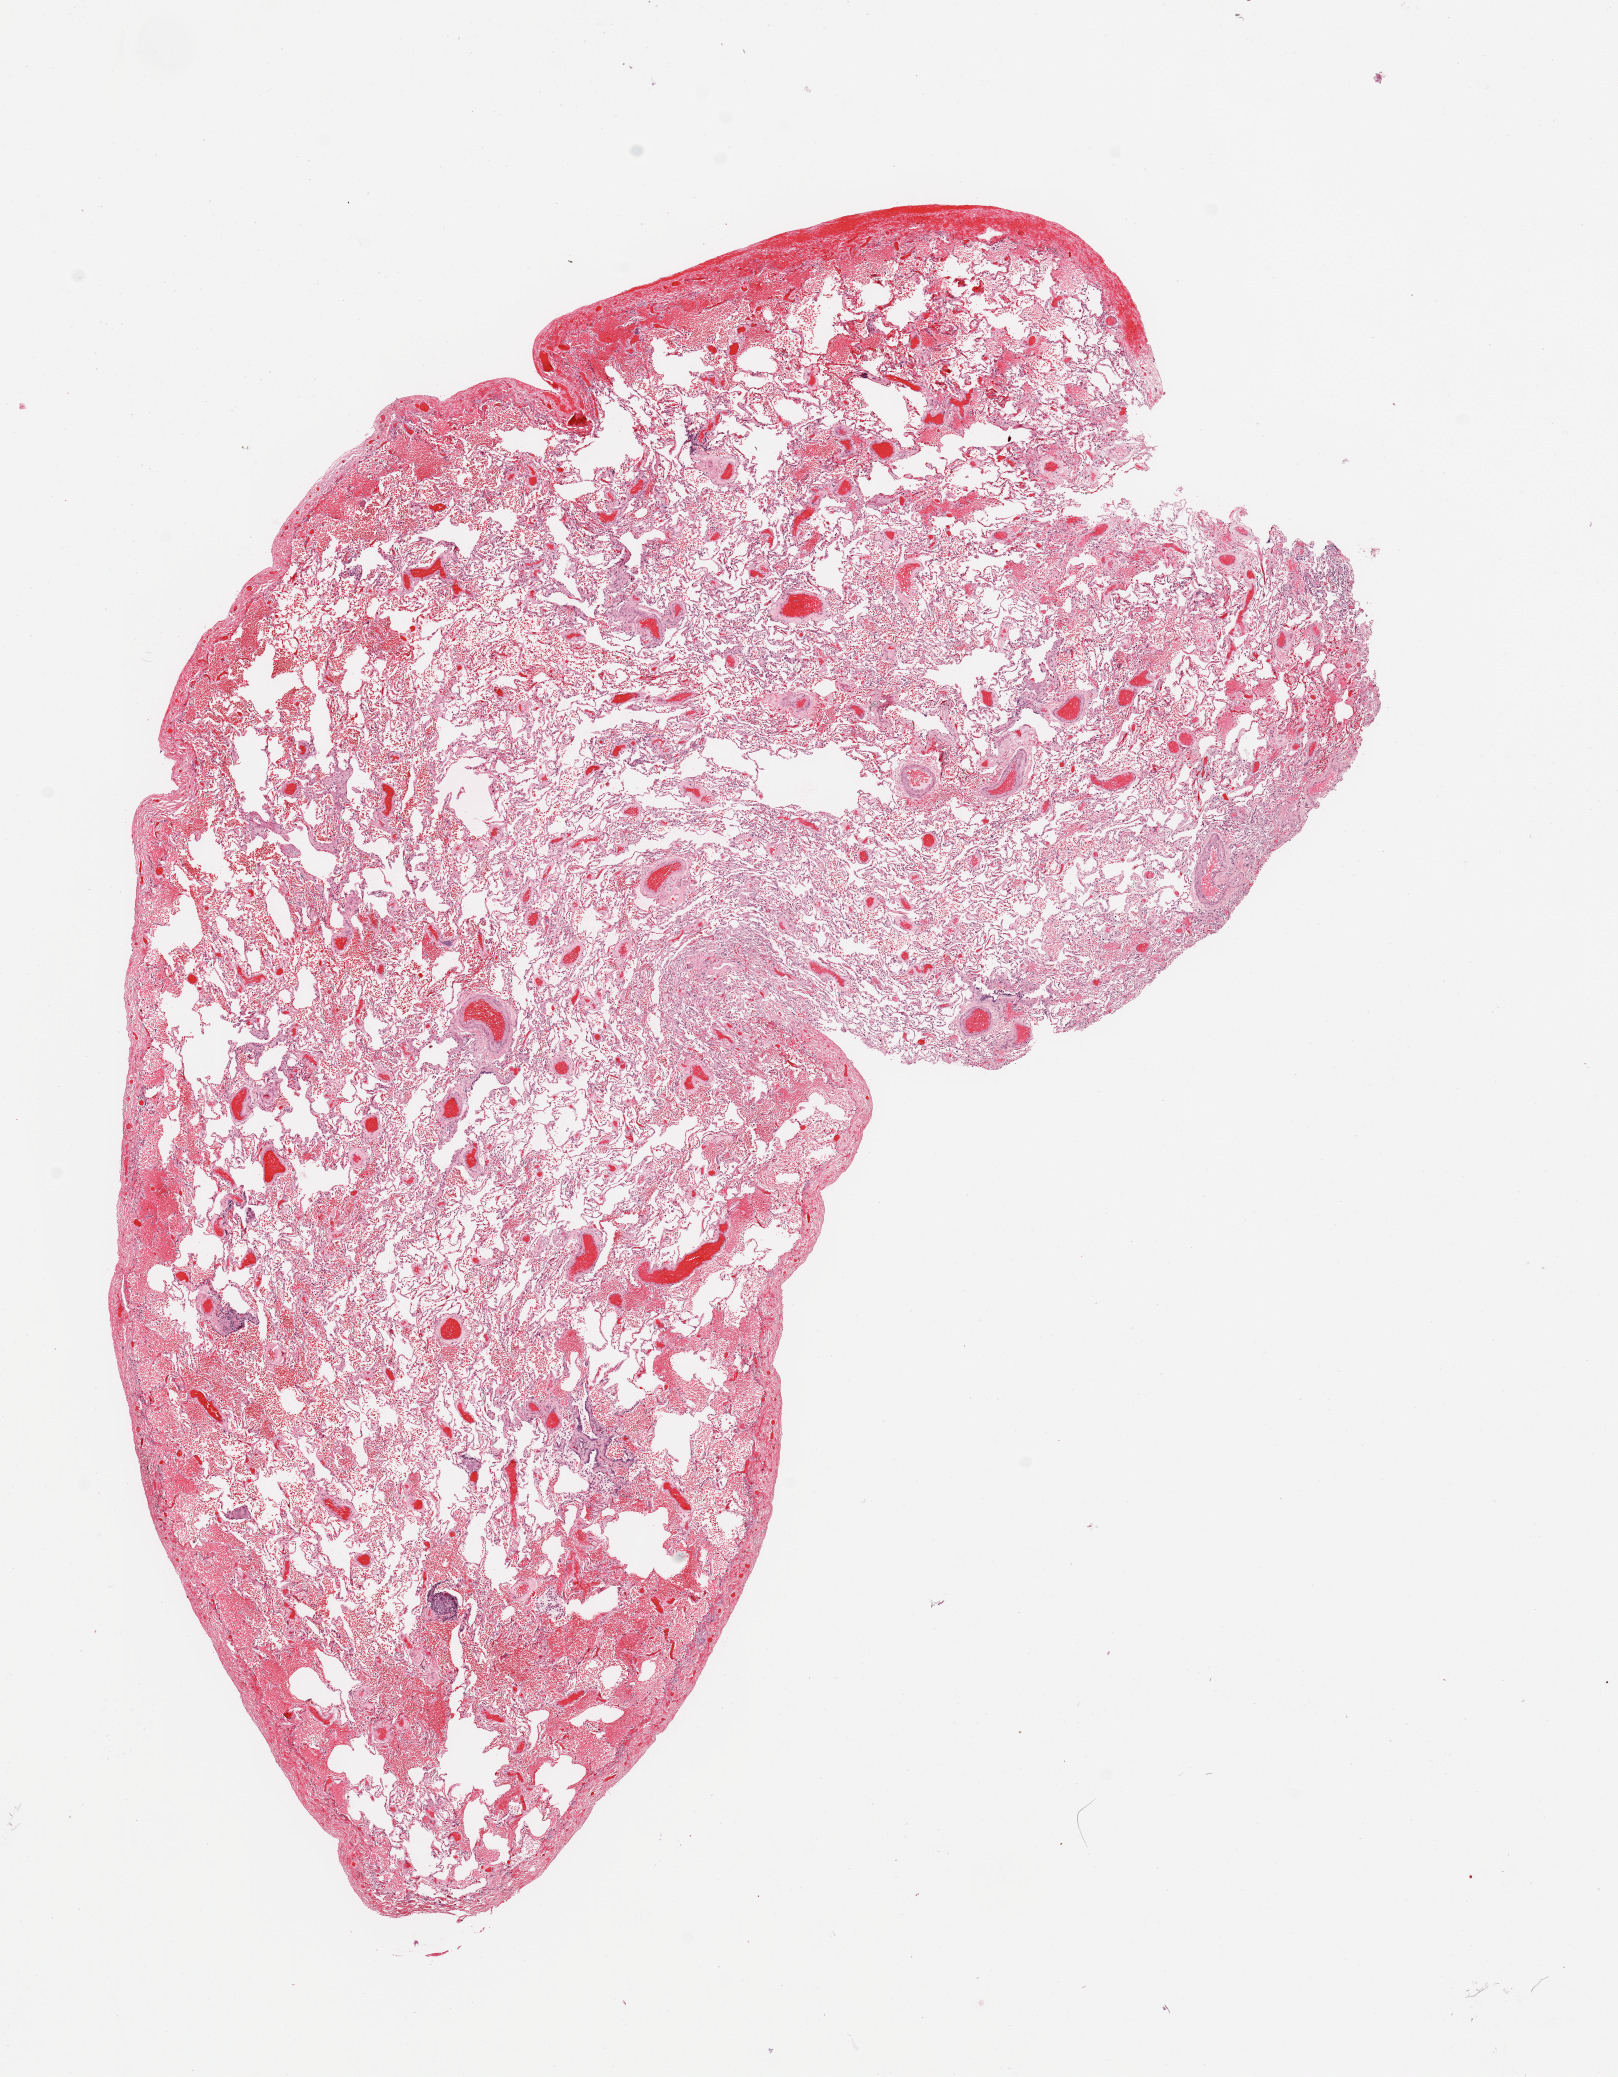
Whole-slide histology image, Hematoxylin and eosin (H&E) stained, low-resolution overview of the scanned area, about 12.8 x 16.4 mm; normal (non-tumour) tissue sample, sampled site: lung. Patient: female, age 72 years.
This section: normal (non-tumour) tissue from the same patient. Patient diagnosis: Adenocarcinoma, NOS.